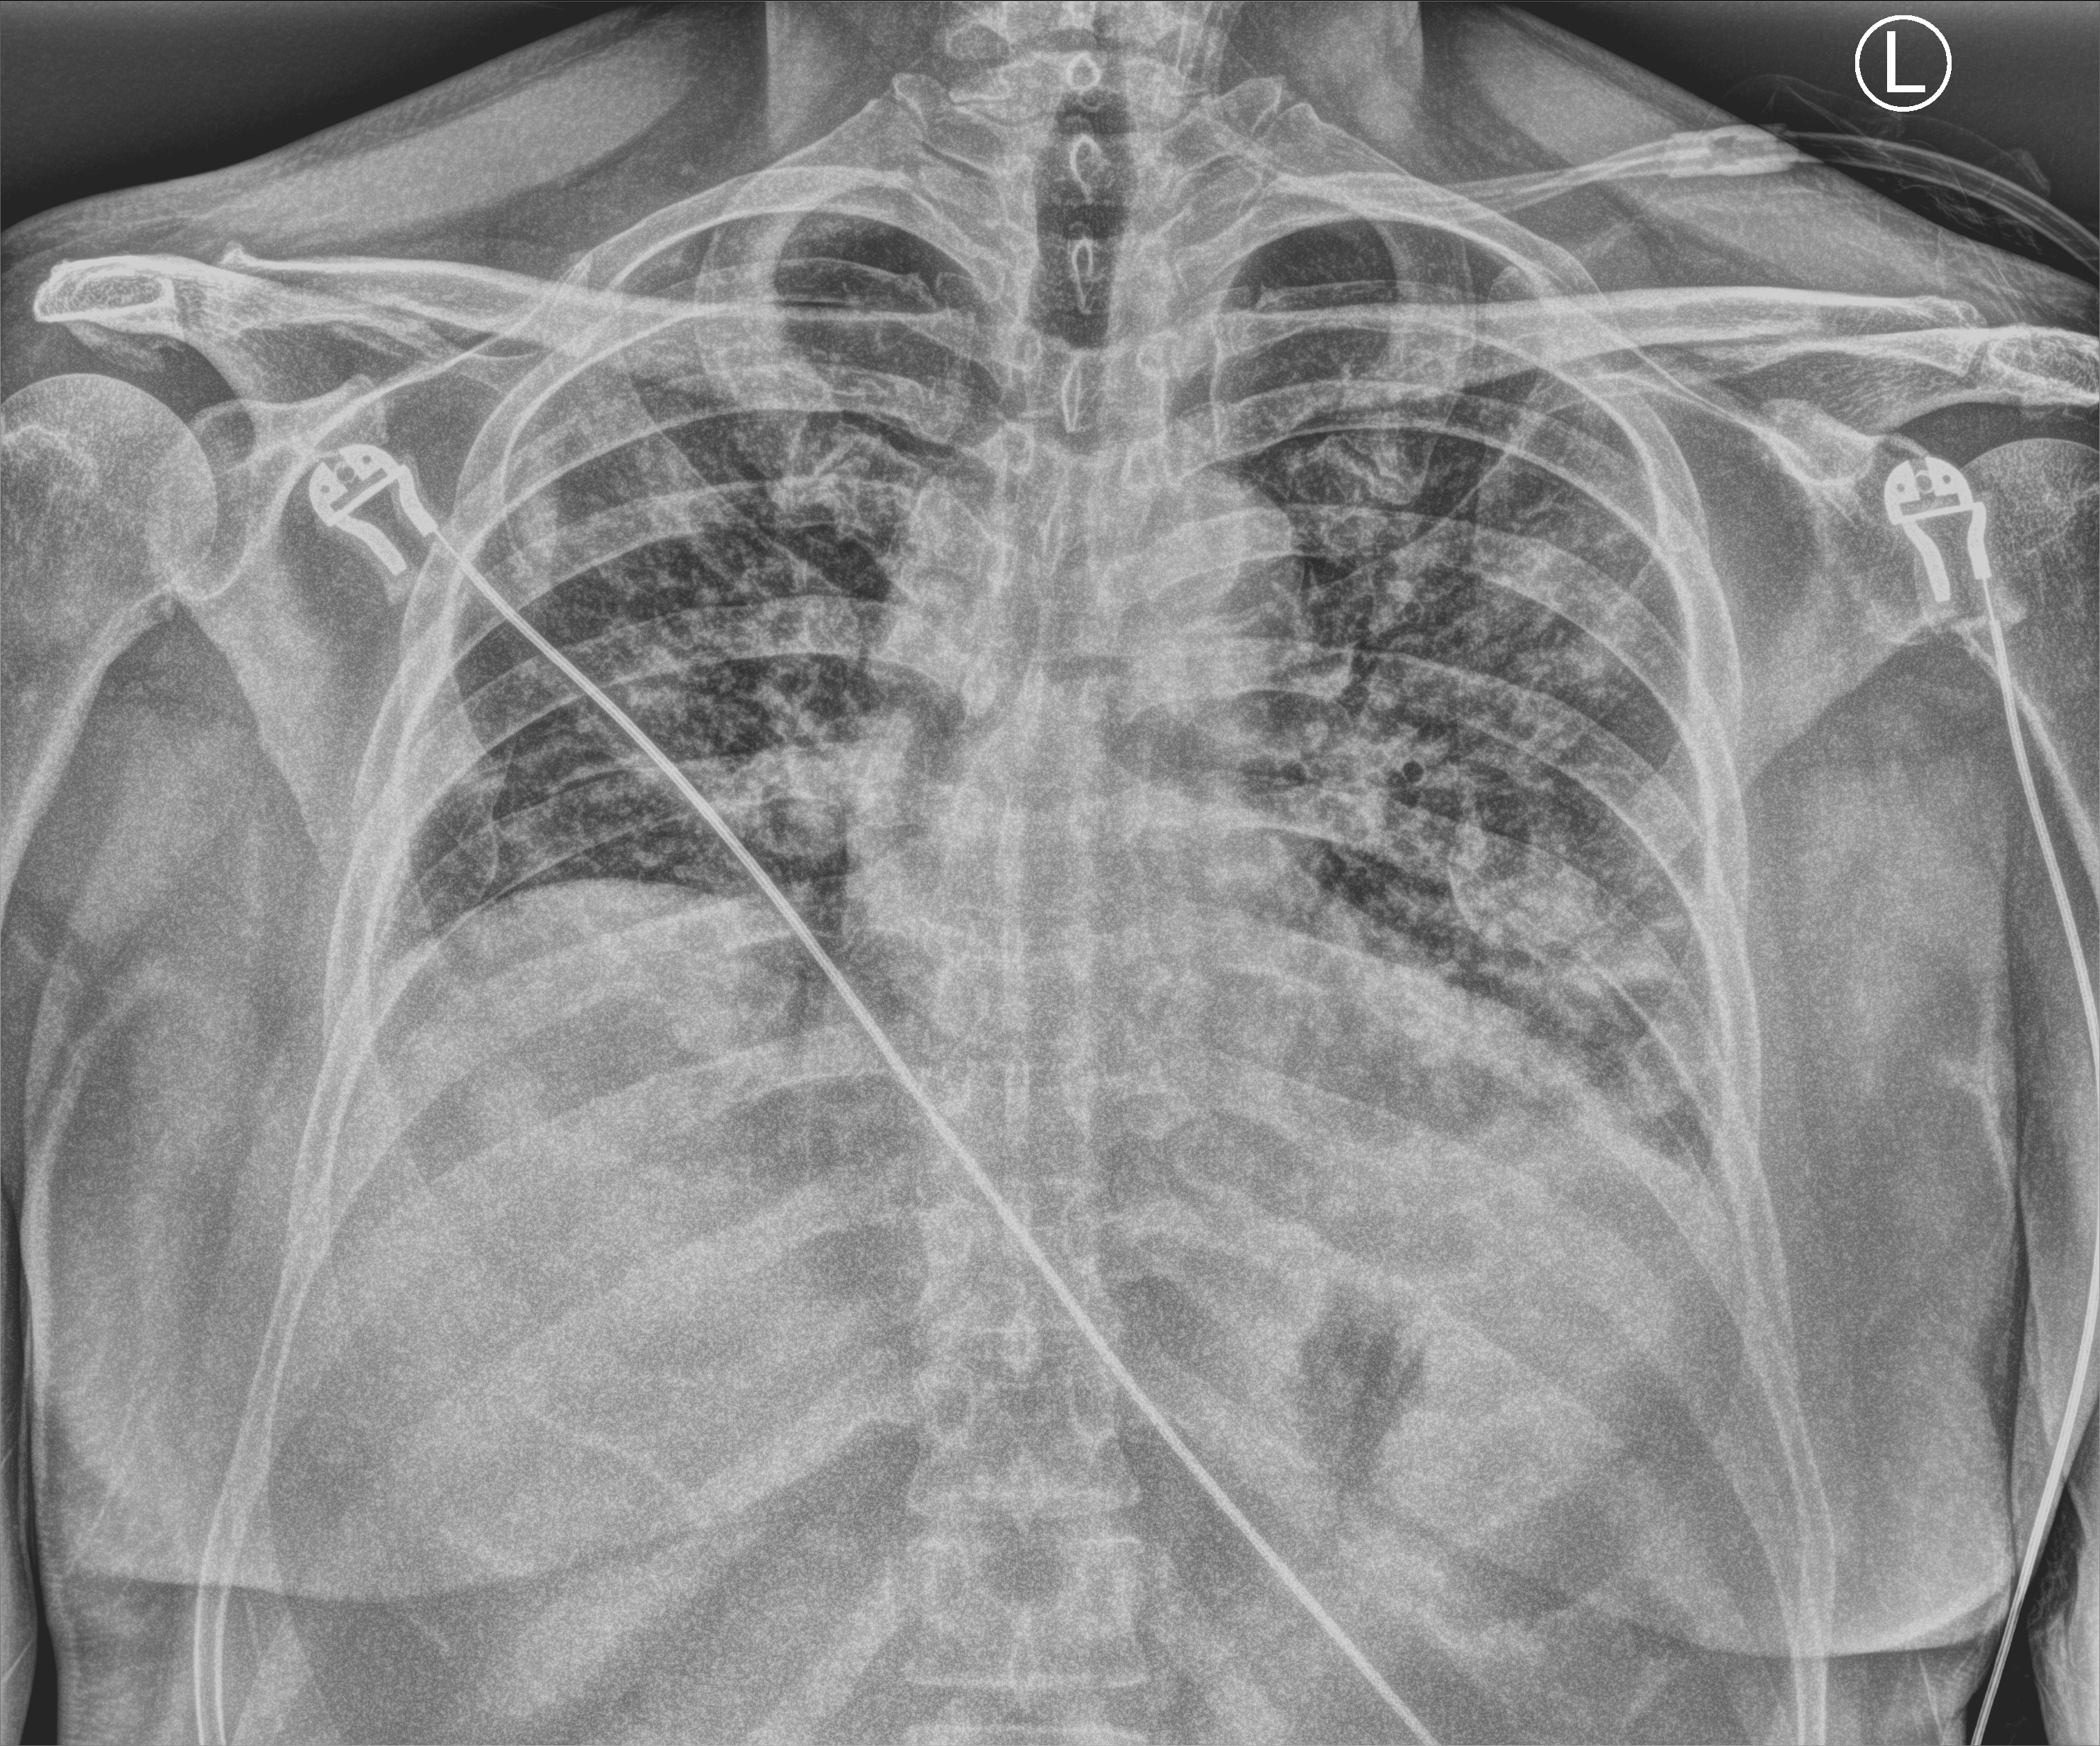
Chest X-ray (portable), anteroposterior (AP) projection. Patient hospitalised with COVID-19; male, aged 18–59 years.
Admission-level facts for this patient (not findings on this image; timing relative to this image not recorded): admitted to intensive care during this hospital stay: no; mechanically ventilated during this hospital stay: no.